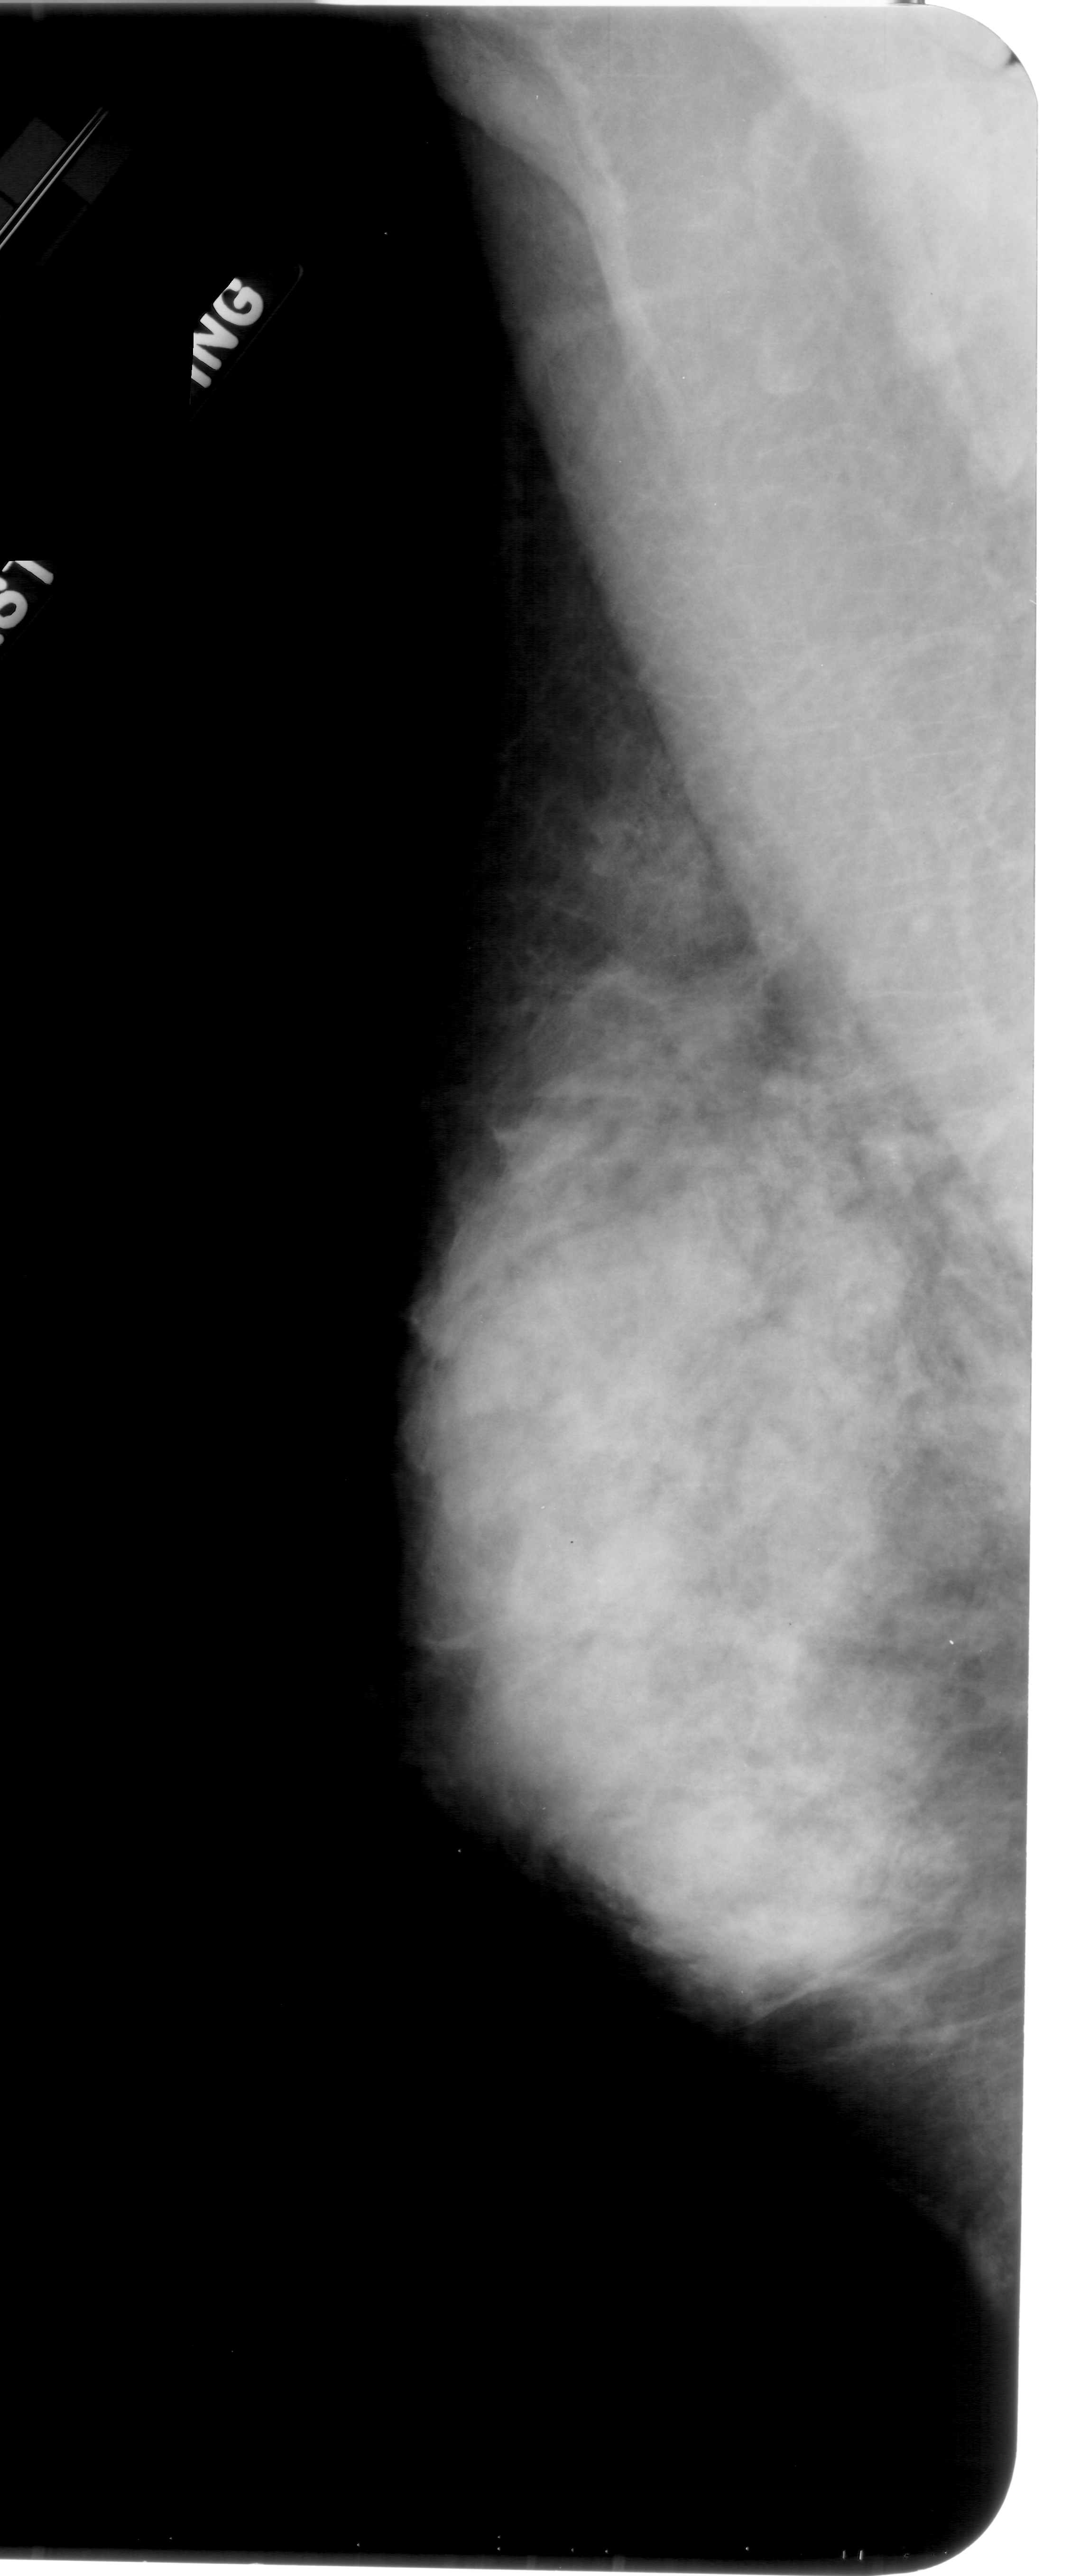
Mammogram (digitized film); left breast; mediolateral oblique (MLO) view; BI-RADS breast density category 4 (scale 1–4); 1089 × 2576 image matrix.
Expert-marked regions of interest on this film, with their recorded descriptors:
- calcifications, morphology pleomorphic, distribution clustered; BI-RADS assessment category 4; pathology result (as recorded, not read from the image): benign: box from (x=875, y=1128) to (x=922, y=1187) px